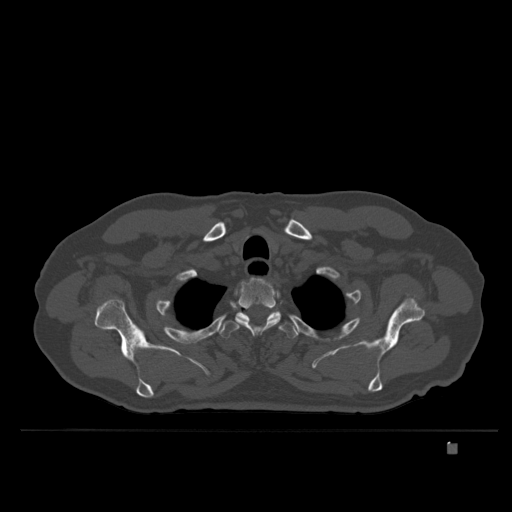
CT including the spine, one axial slice. Slice 308 of 435 in the series (ordered by position). Bone window (W 1800 / L 400 HU). 1.5 mm slice thickness. 512 × 512 image matrix, field of view 434 × 434 mm. Patient: male, 73 years. Case-level facts recorded for this patient, not image findings: primary cancer: skin.
Annotated regions visible in this slice (semi-automatic segmentation, software-assisted and operator-edited):
- T2 vertebra: bounding box [x1, y1, x2, y2] px = [235, 278, 281, 335]
- T3 vertebra: [219, 309, 299, 339]